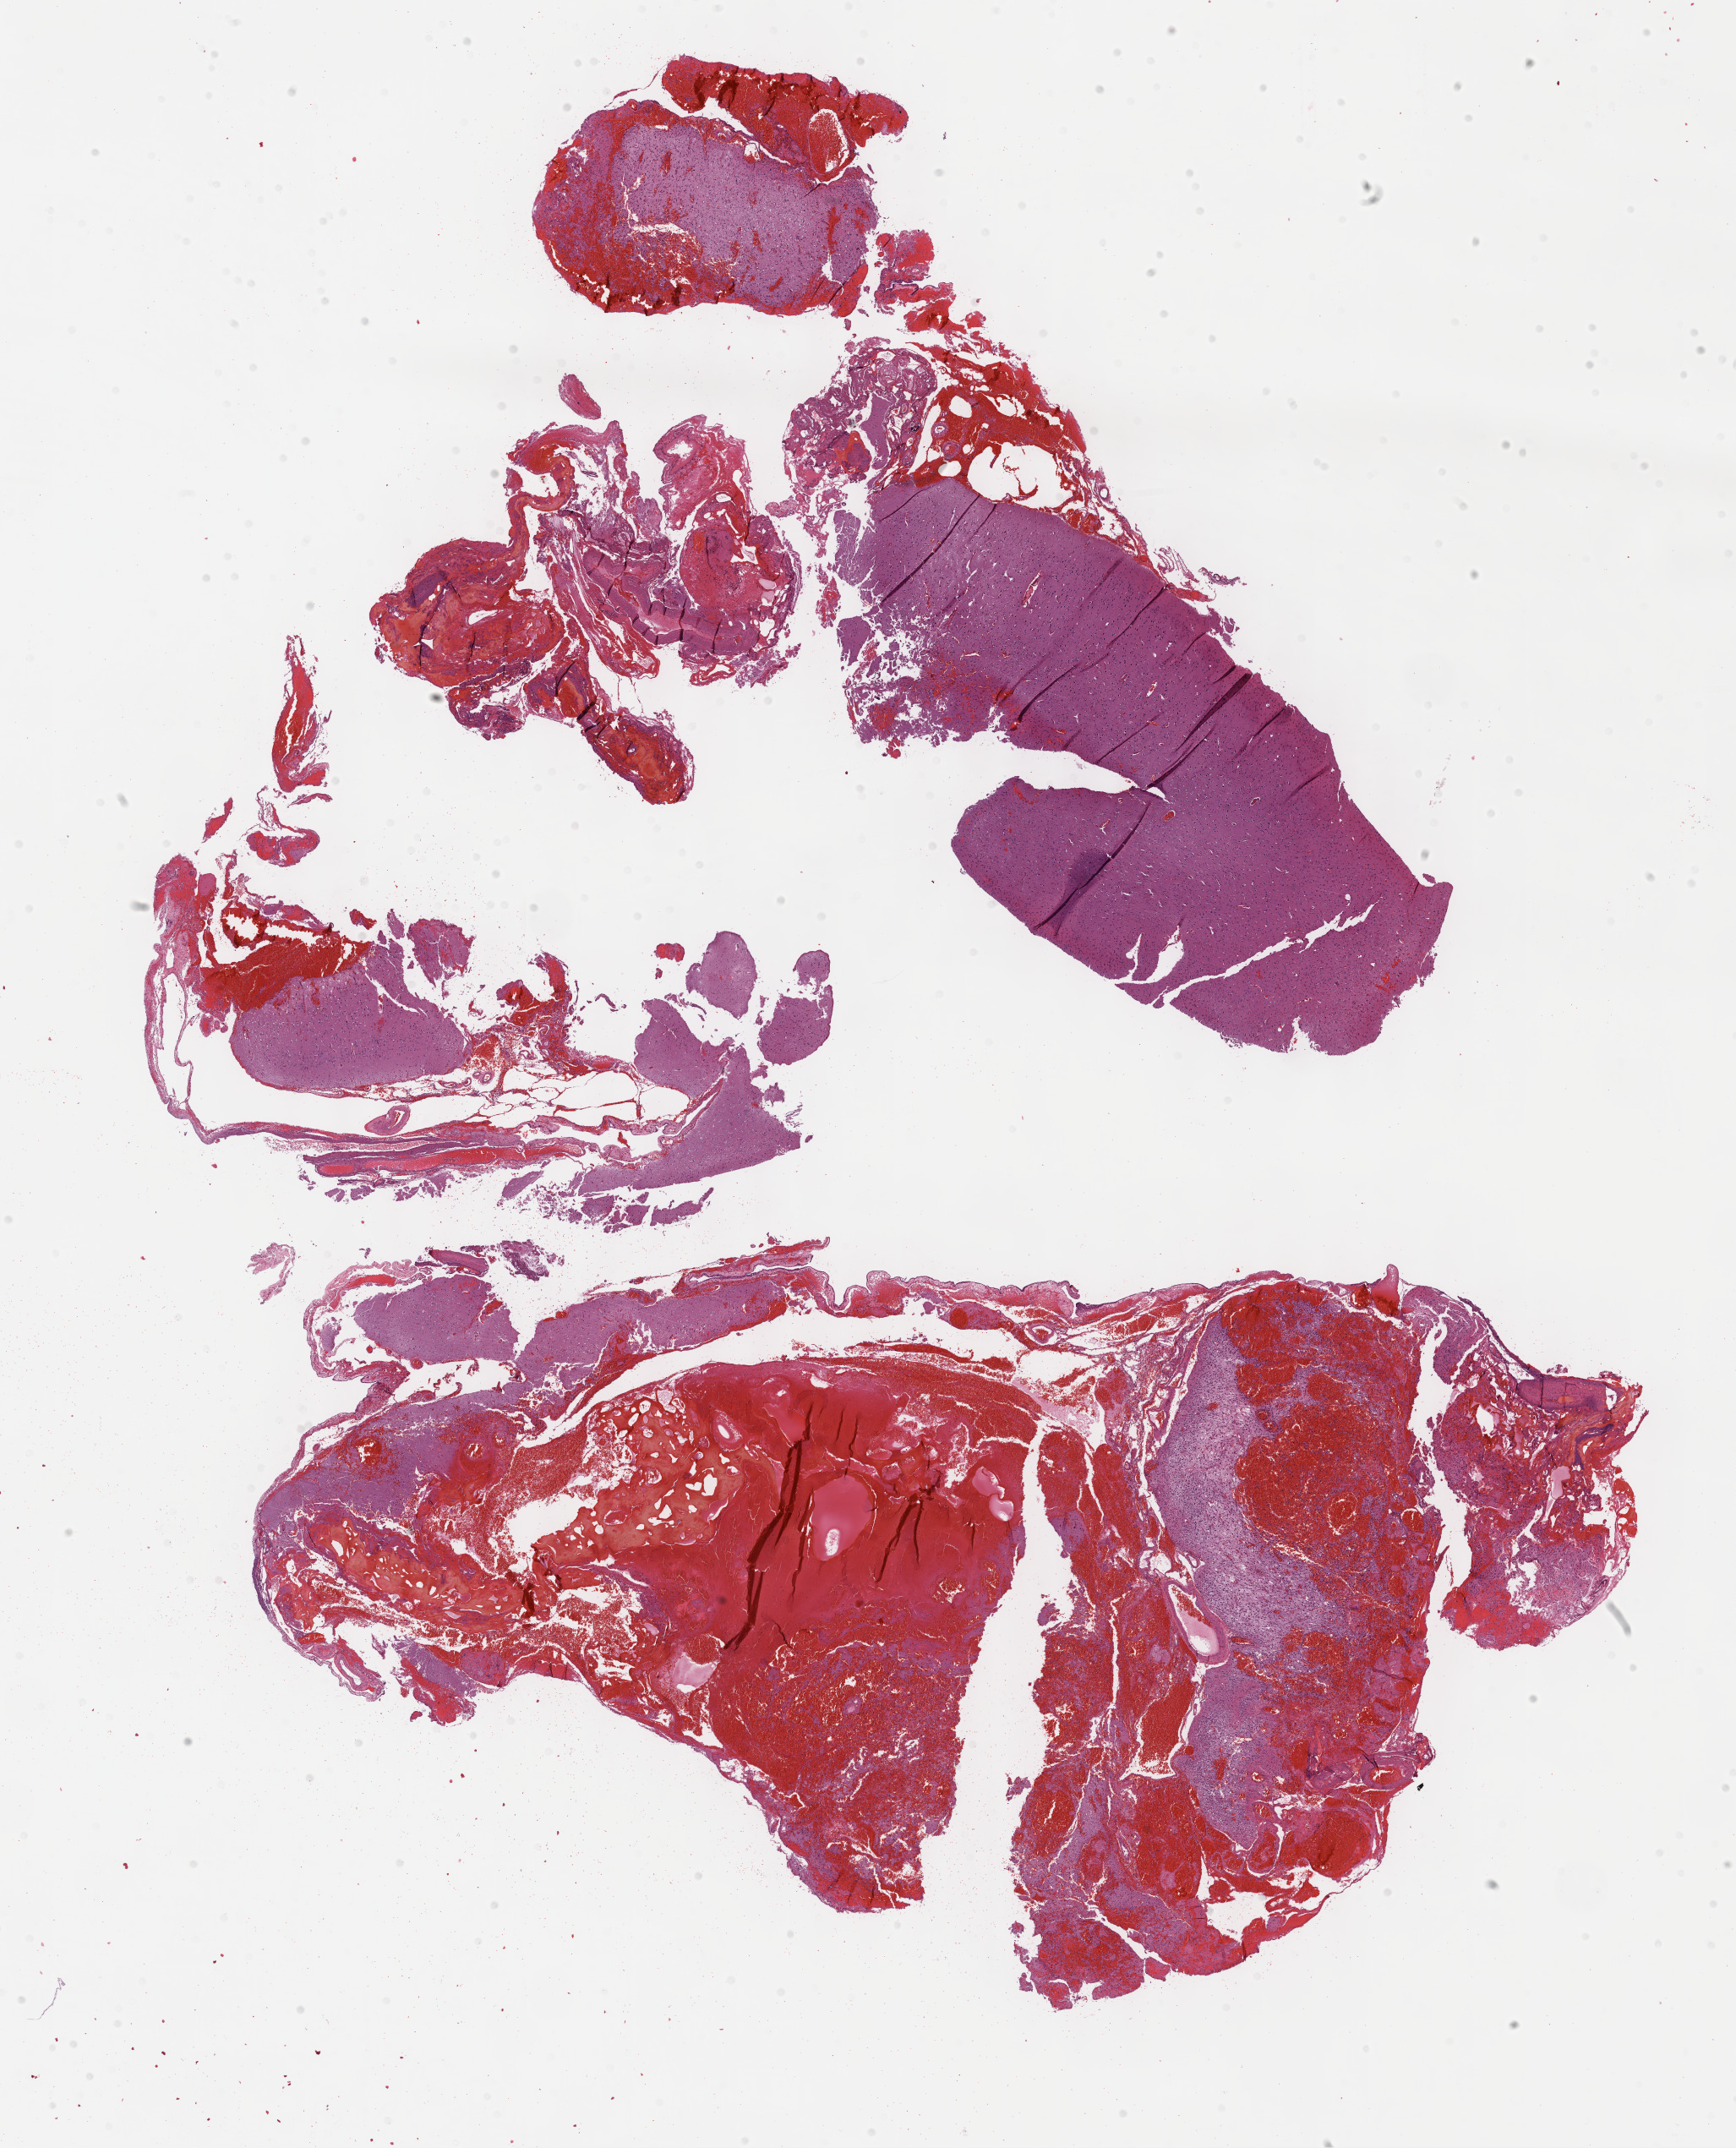
H&E-stained whole-slide image, low-resolution overview of the scanned area, about 16.6 x 20.5 mm (slide scanned at 40x); formalin-fixed paraffin-embedded (FFPE) diagnostic section; sample: primary tumour, brain. Patient: male, age at initial diagnosis 14 years. Histologic grade: G2 (moderately differentiated).
• pathologic diagnosis: Mixed glioma (cerebrum)
• laterality: right